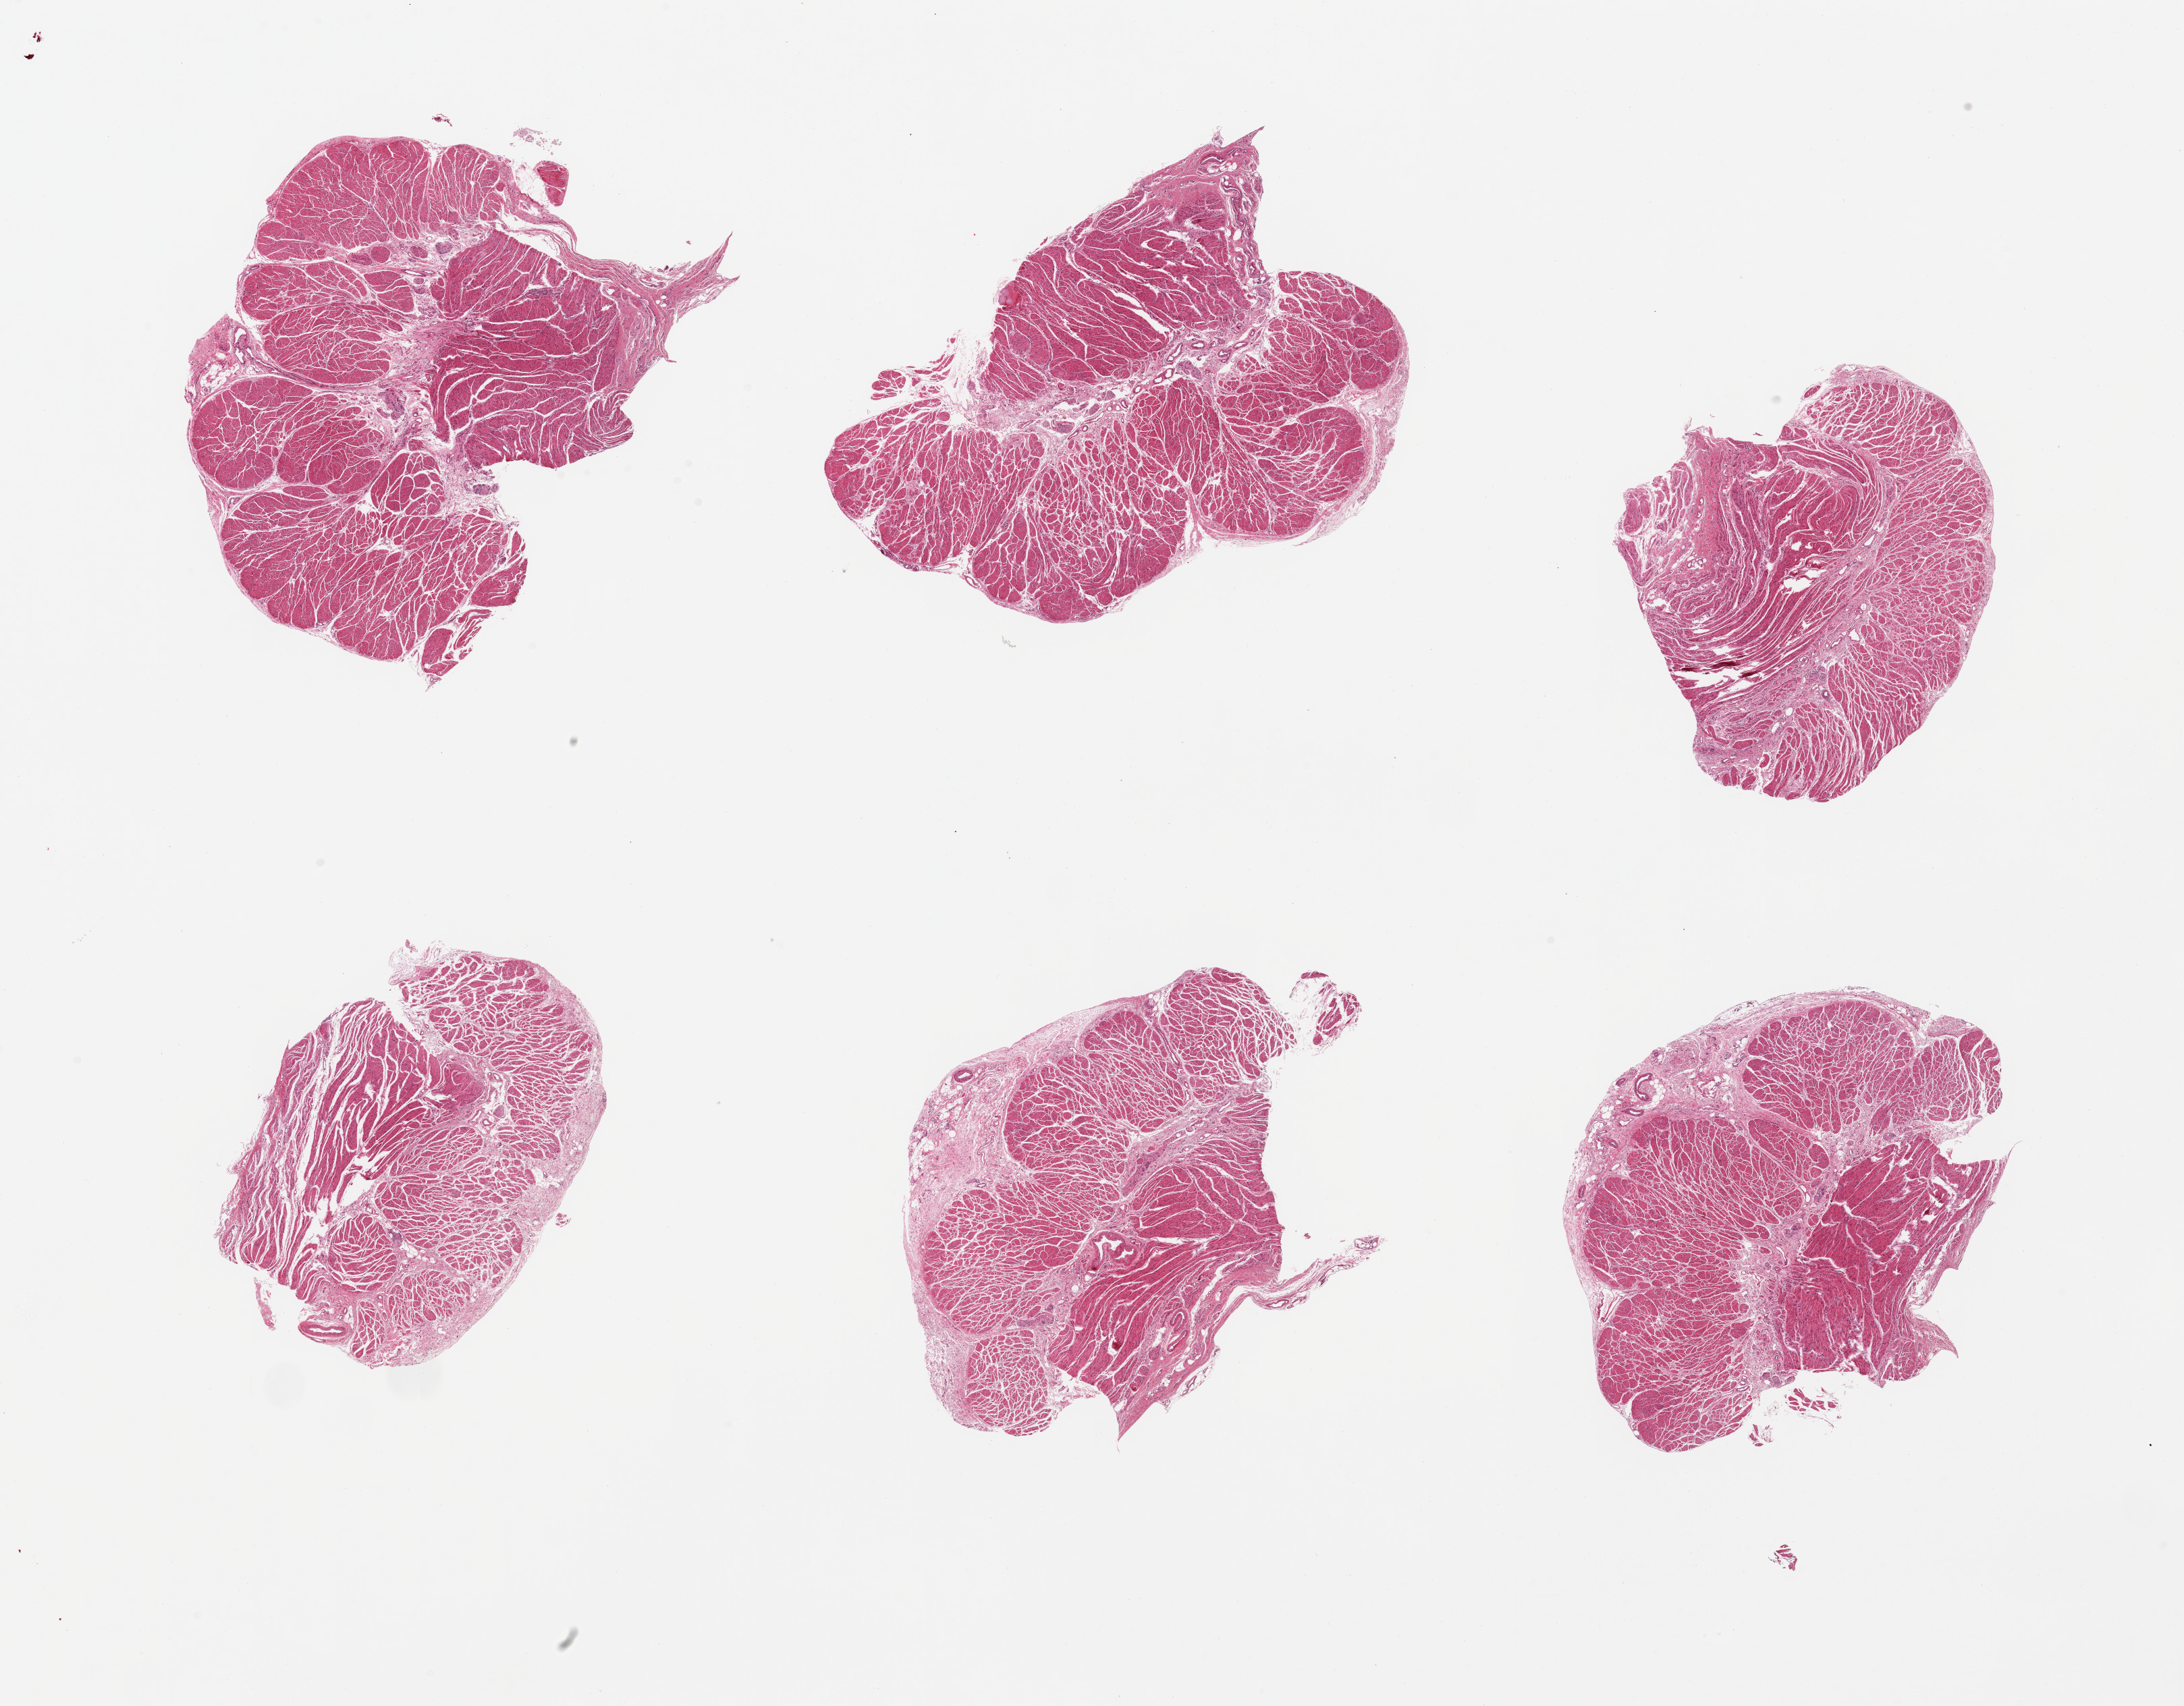
Hematoxylin and eosin (H&E) whole-slide image, a low-resolution overview of the entire scanned area, about 25.6 x 20.0 mm (from a 20x scan). PAXgene-fixed paraffin-embedded (PFPE) section. Sampled site (target tissue): gastroesophageal junction. Tissue donor sample. Donor sex: female.
Reviewer comment on this tissue sample: 6 pieces, target muscularis, good specimen.